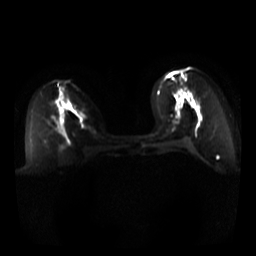
Breast MRI, one axial slice; diffusion-weighted series; image 2 of 4 stored at this slice position (different b-values; order by instance number); 3 T; 5 mm slice thickness; 256 × 256 image matrix, field of view 340 × 340 mm. Female patient.
Outlined on this slice (manually delineated by an expert):
- tumour on diffusion-weighted imaging: bounding box (x1, y1, x2, y2) in pixels: (180, 97, 183, 104)